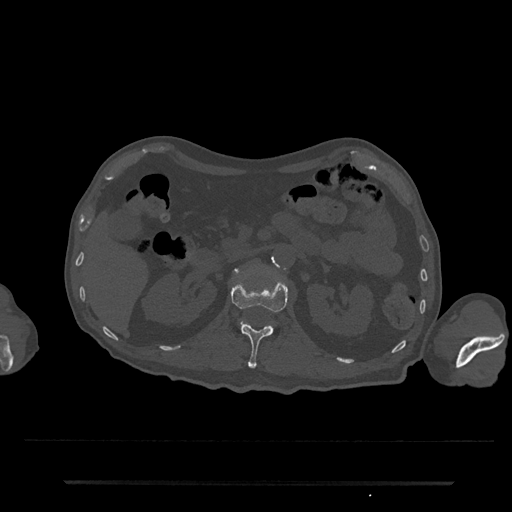
CT including the spine, one axial slice; slice 113 of 797 in the series (ordered by position); reconstruction kernel Br40s/3; 120 kVp; bone window (W 1800 / L 400 HU); 0.5 mm slice thickness; 512 × 512 image matrix, field of view 427 × 427 mm. Patient: male, 74 years. From the clinical record (not read from this slice): primary cancer: prostate.
Structures marked on this image (semi-automatic segmentation, software-assisted and operator-edited):
- L1 vertebra: bounding box (x1, y1, x2, y2) in pixels: (231, 276, 288, 369)